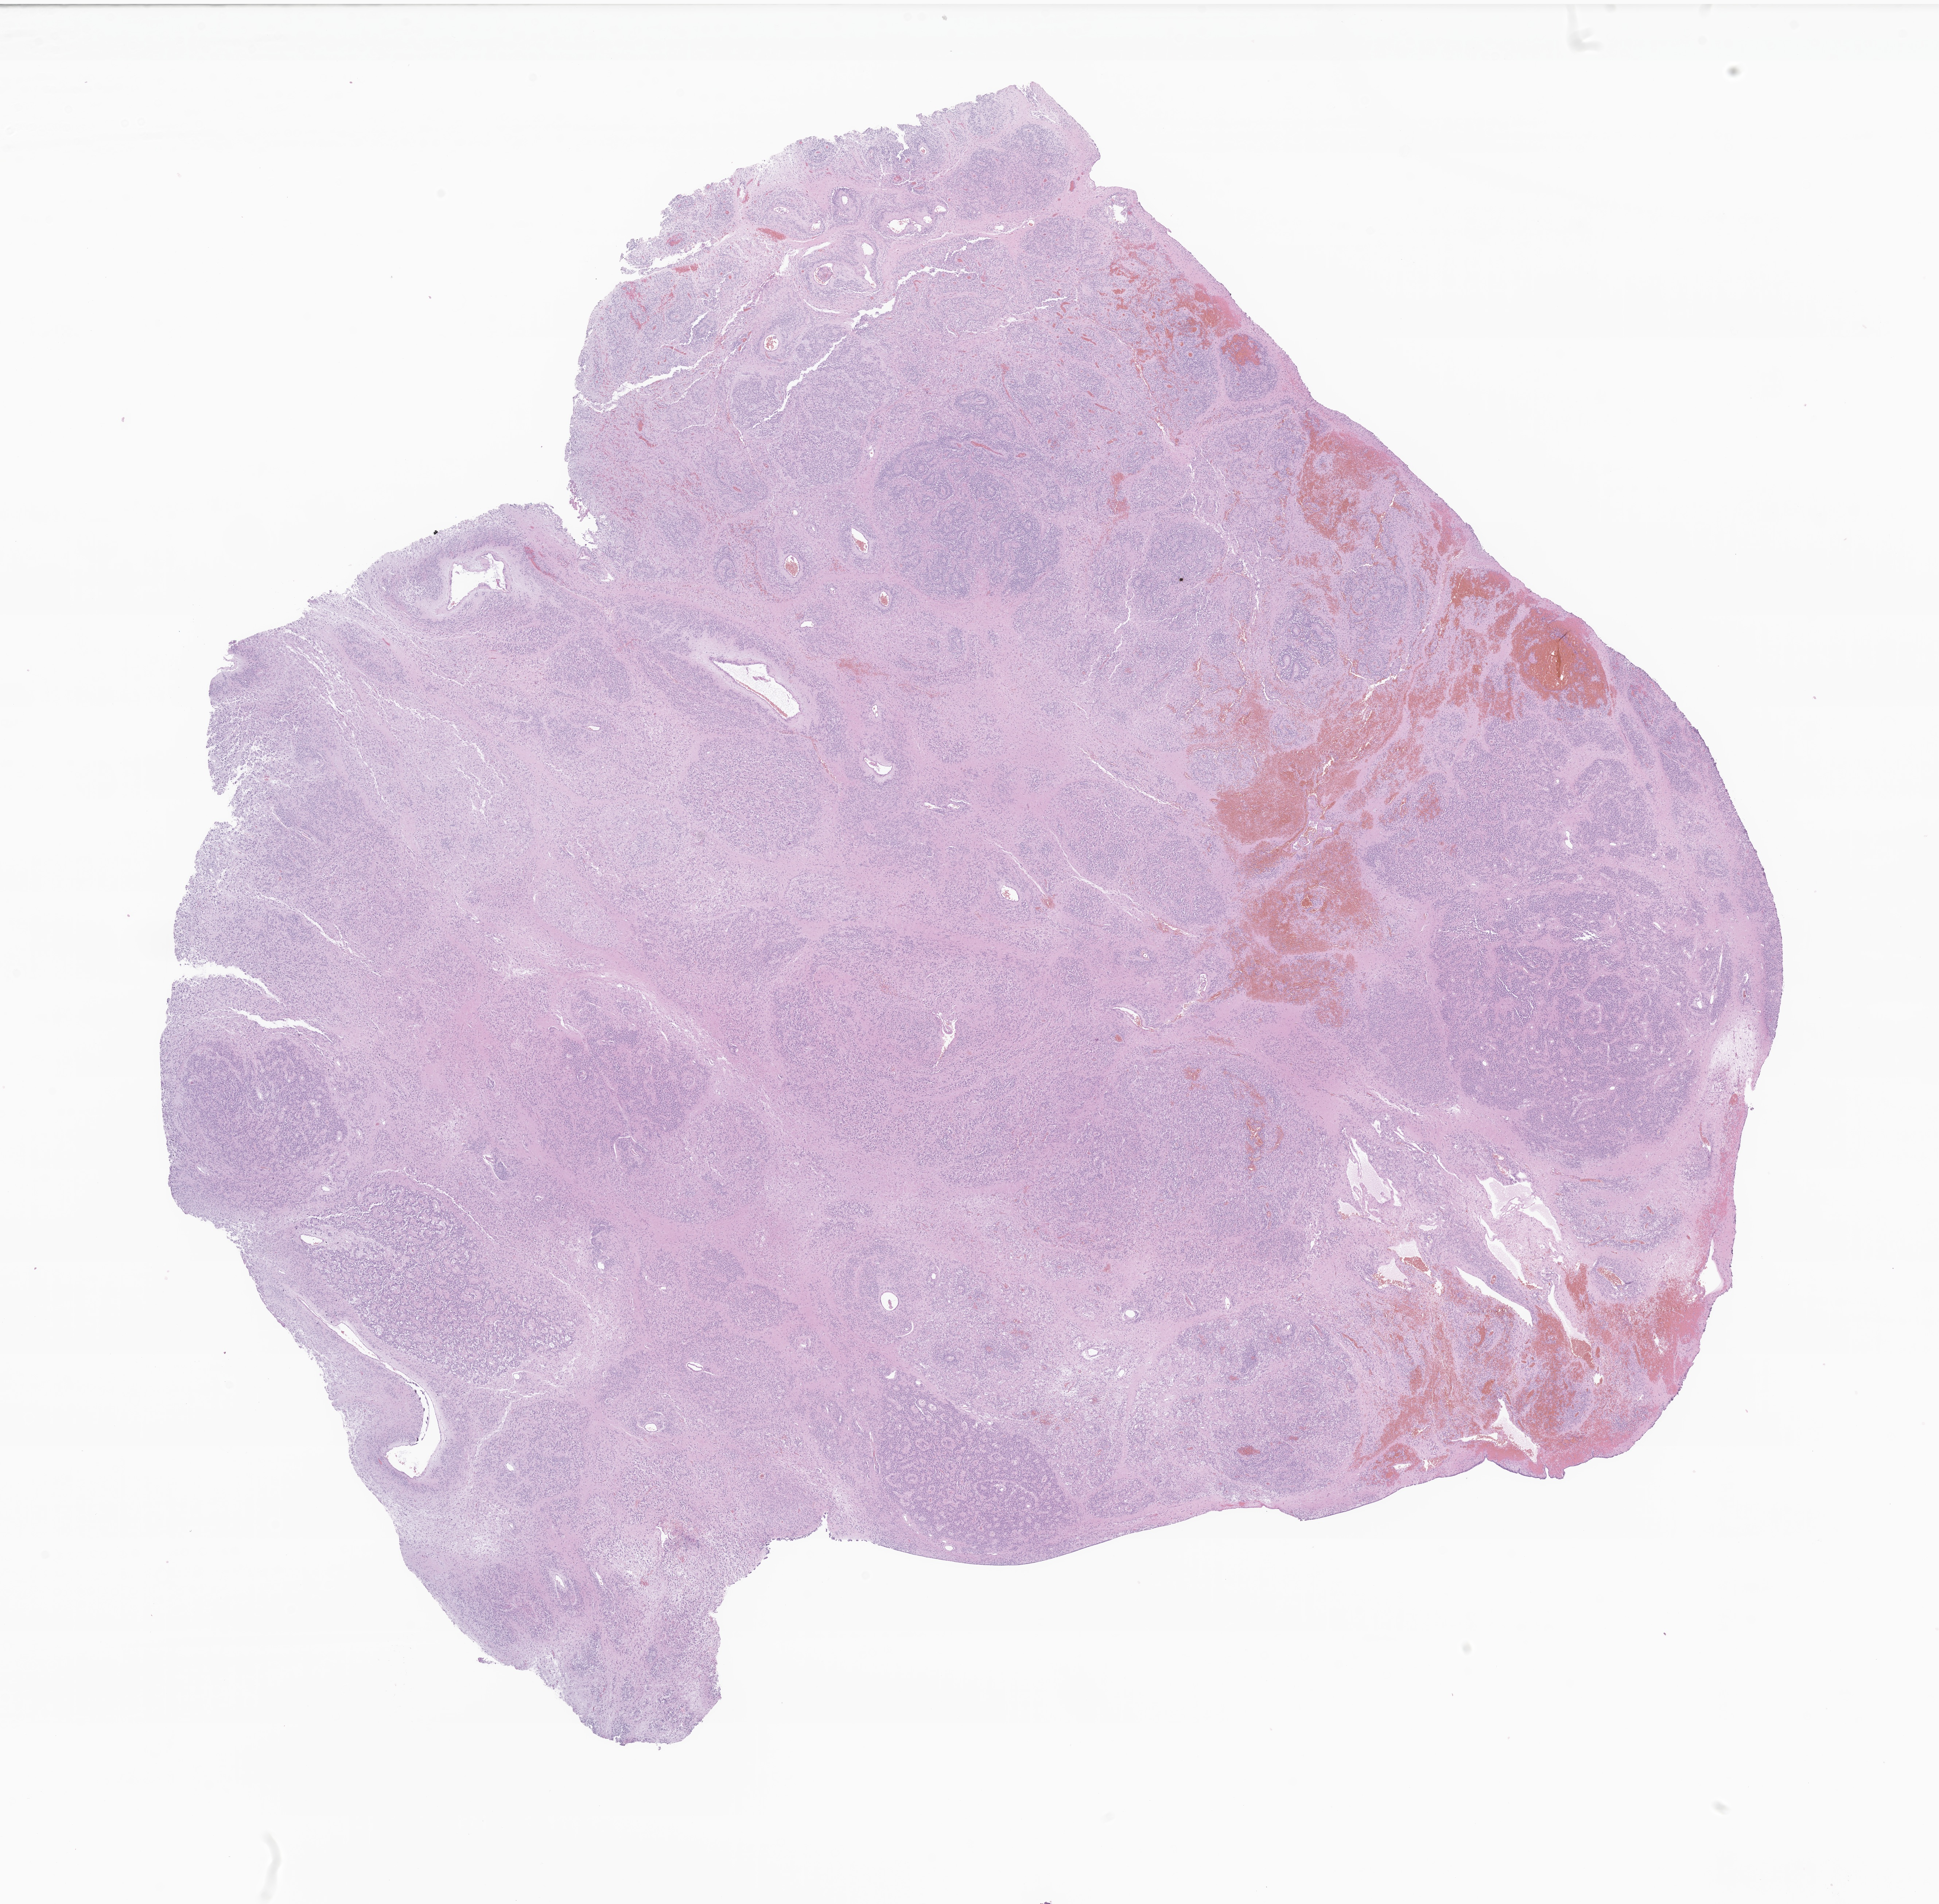
Digitized haematoxylin and eosin-stained section of tumor tissue from the brain — a low-resolution overview of the entire scanned area, about 22.4 x 22.0 mm; formalin-fixed, paraffin-embedded (FFPE) tissue. Patient: male, age 503 days (about 1.4 years).
Diagnosis (ICD-O-3 morphology term): Ependymoma, NOS.